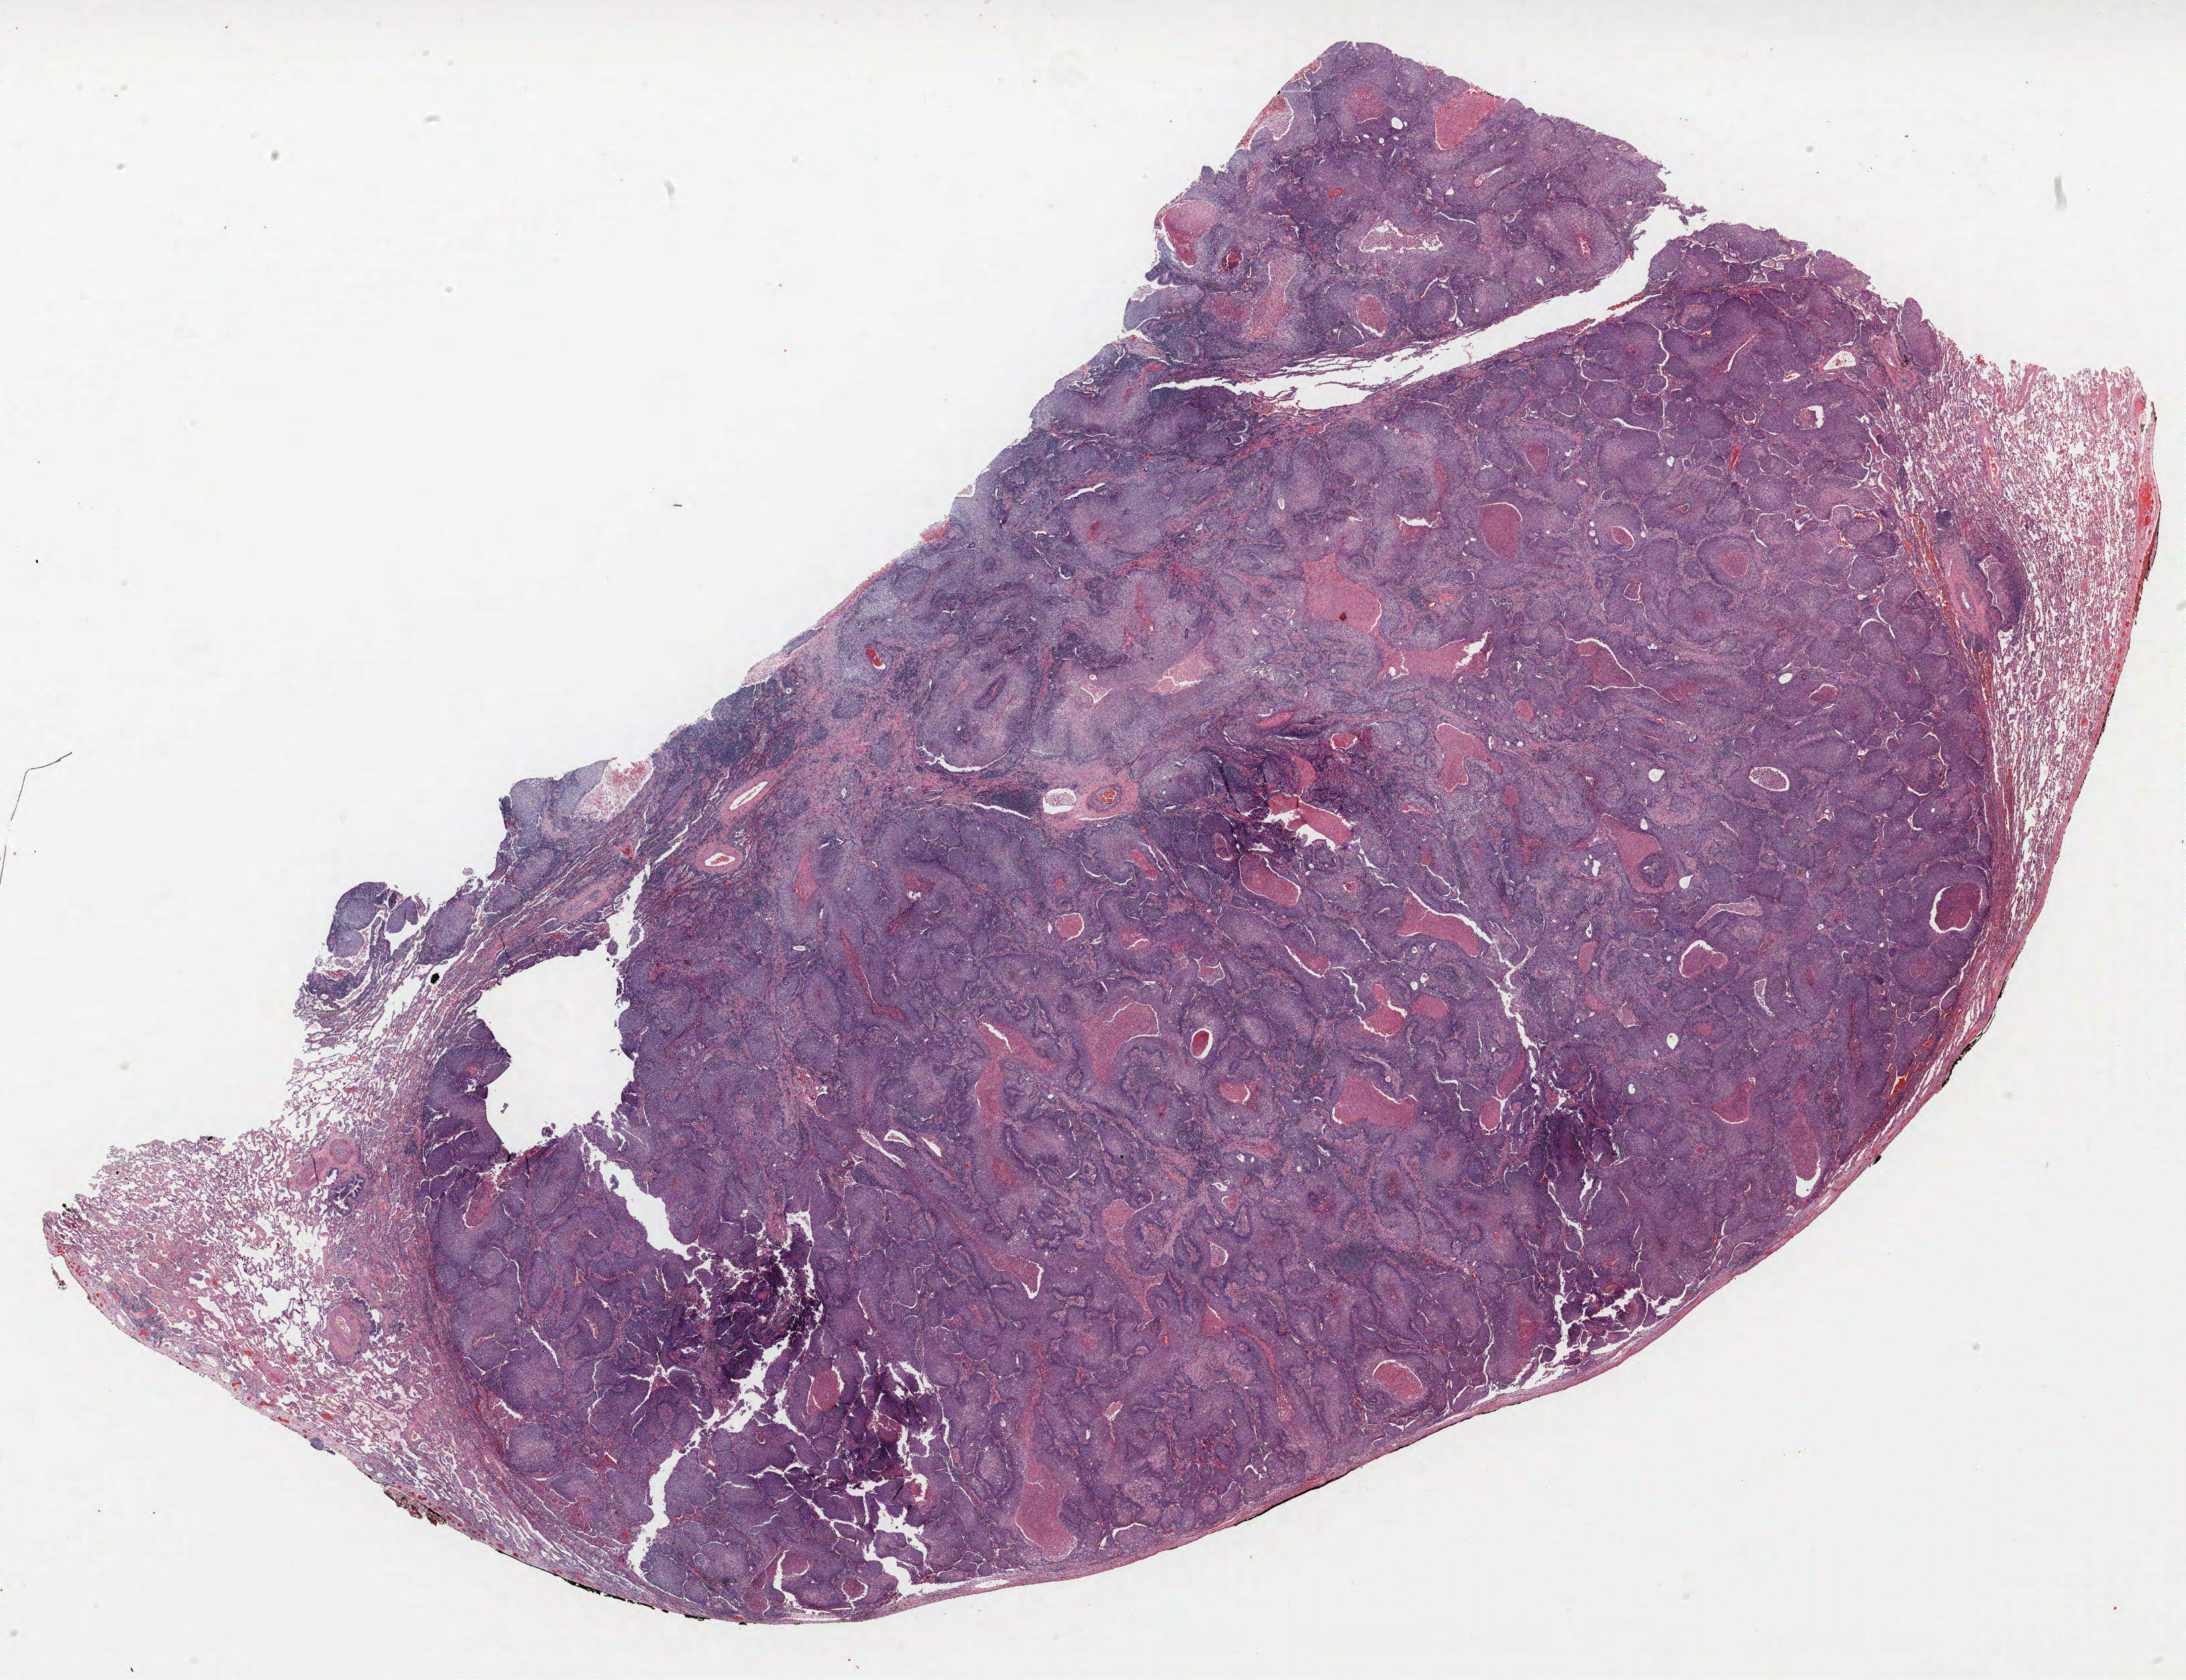
H&E-stained whole-slide image — whole scanned area (about 26.4 x 20.3 mm, from a 40x scan) shown as a low-resolution overview; formalin-fixed paraffin-embedded (FFPE) section; lung. Male patient, aged 59 at enrolment. Current smoker at enrolment. Grade: moderately differentiated (G2).
Primary tumour location (clinical record): right upper lobe, right middle lobe. Tumour size (pathology): 13 mm. Participant's lung-cancer diagnosis: Adenocarcinoma, NOS. Stage (AJCC 6th edition): IA. Note: participant had 2 primary lung cancers recorded; fields above describe the first.